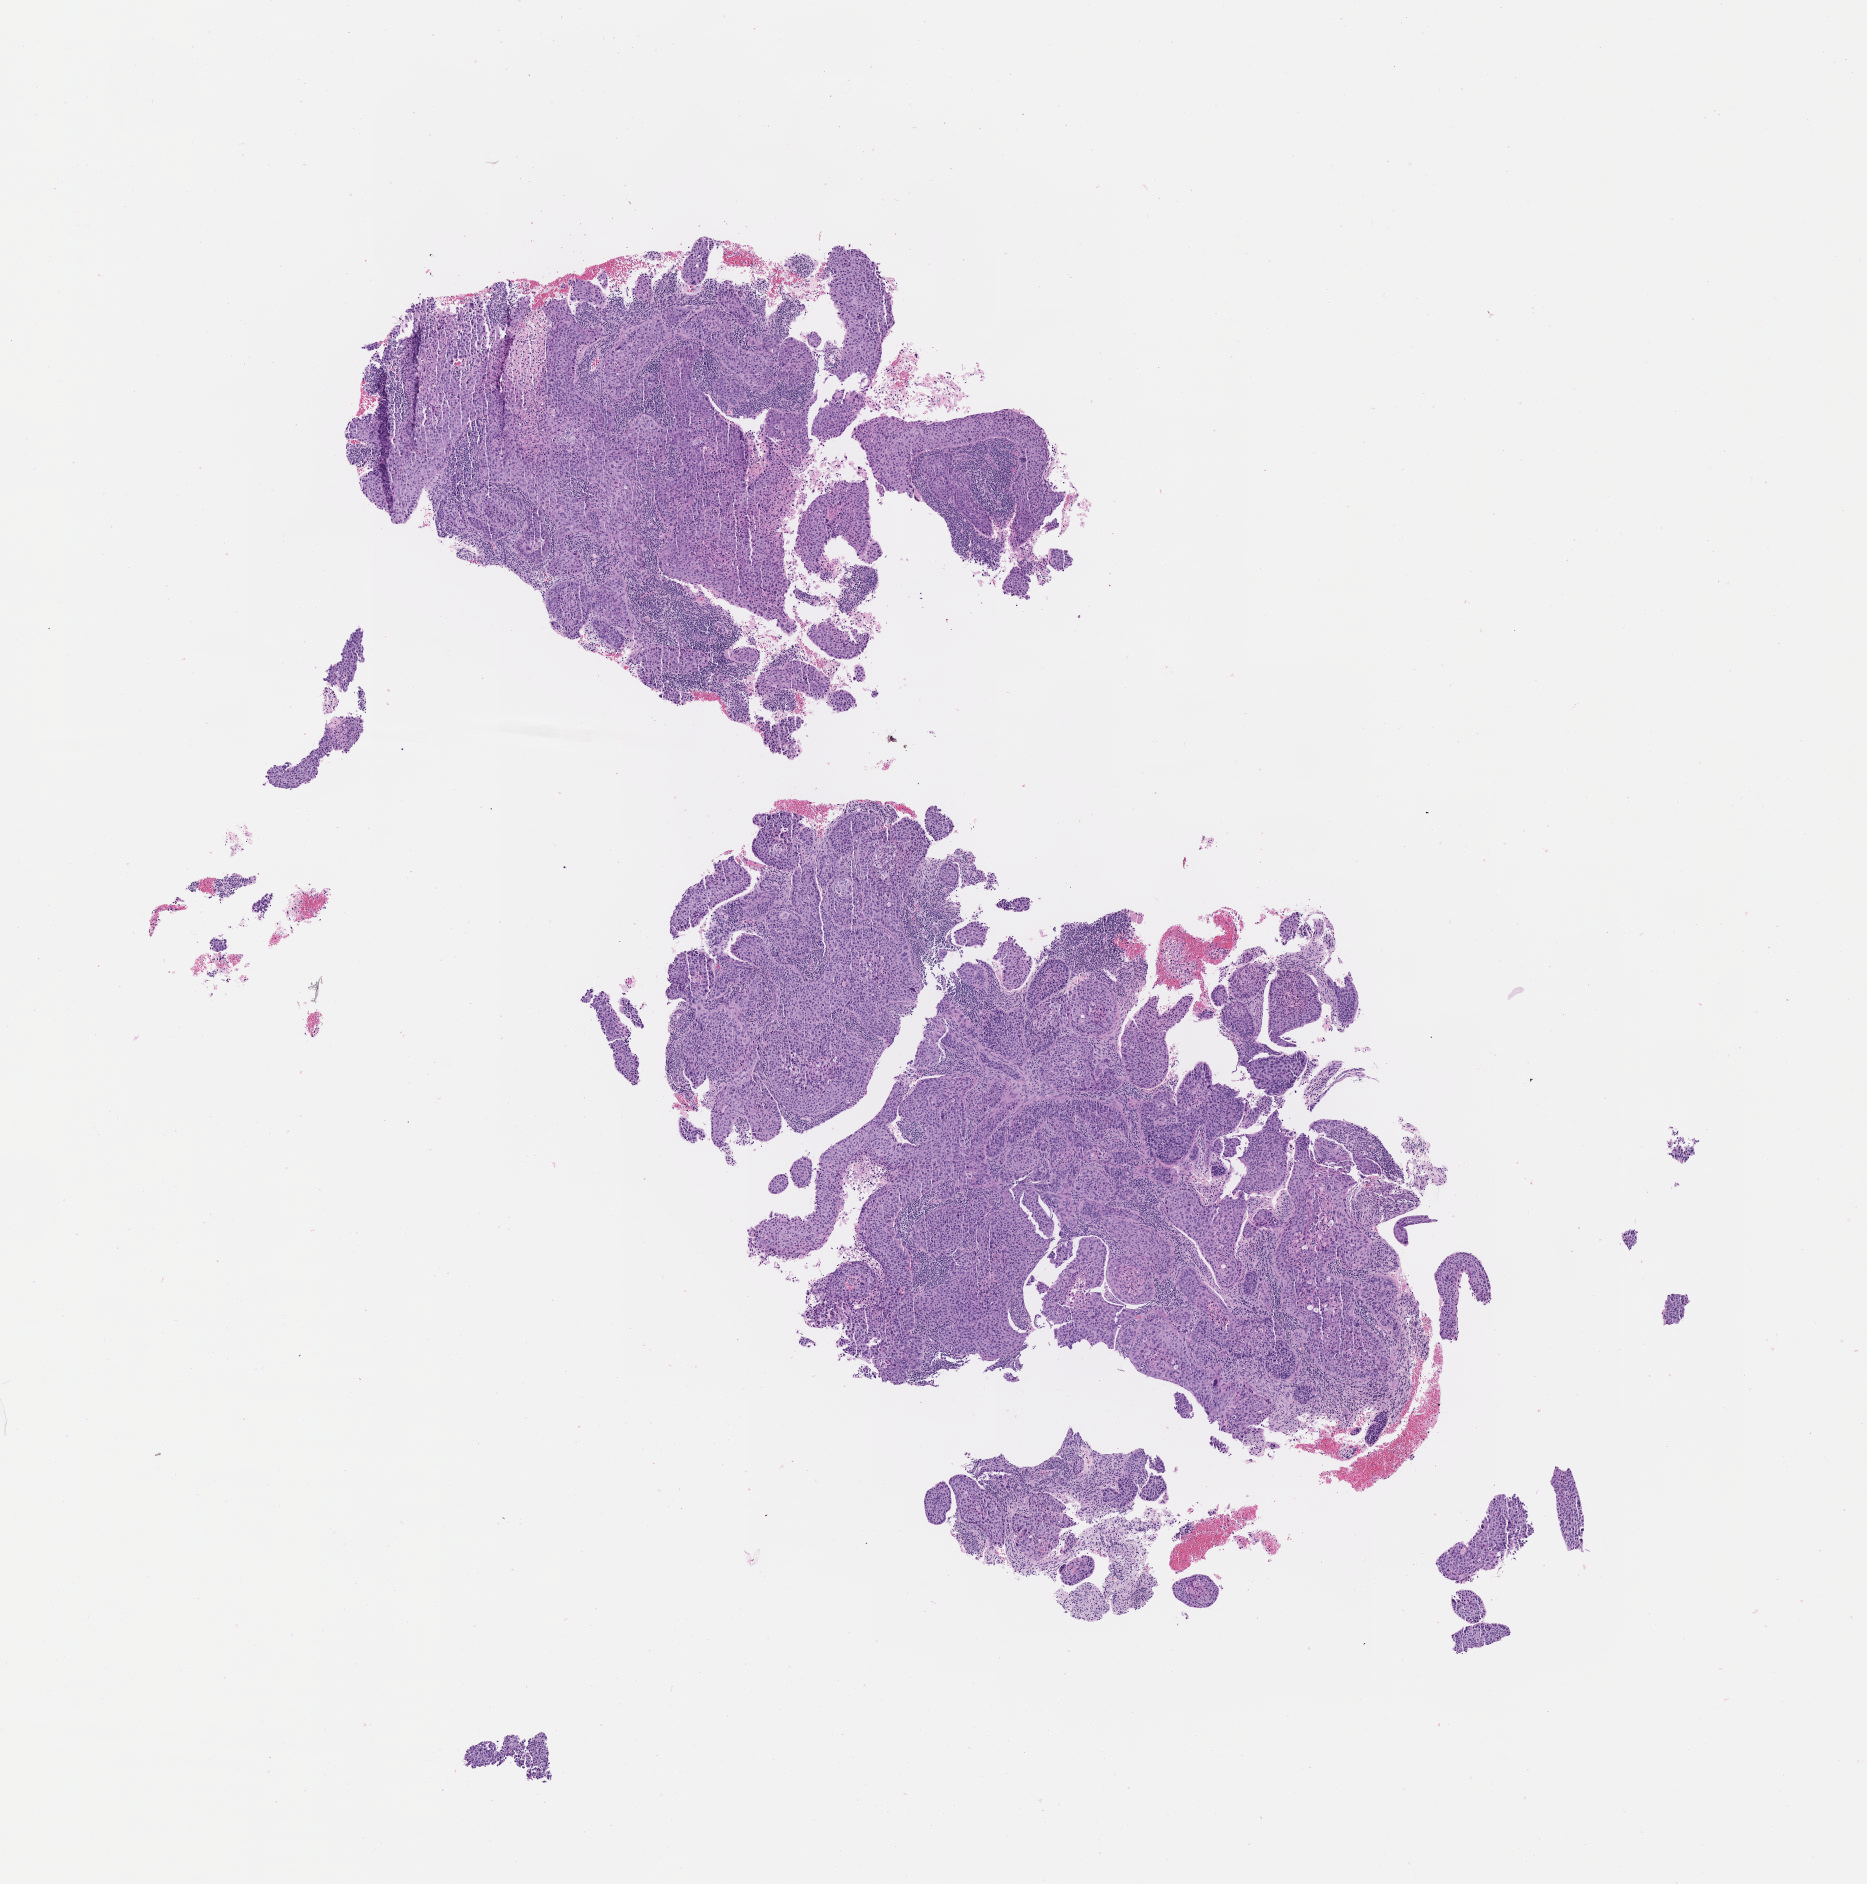
Digitized hematoxylin and eosin (H&E)-stained section, whole scanned area (about 7.5 x 7.6 mm) shown as a low-resolution overview; specimen: tumor tissue; anatomic site: cervix. Female patient, 41 years old.
* diagnosis: Squamous cell carcinoma, large cell, nonkeratinizing, NOS